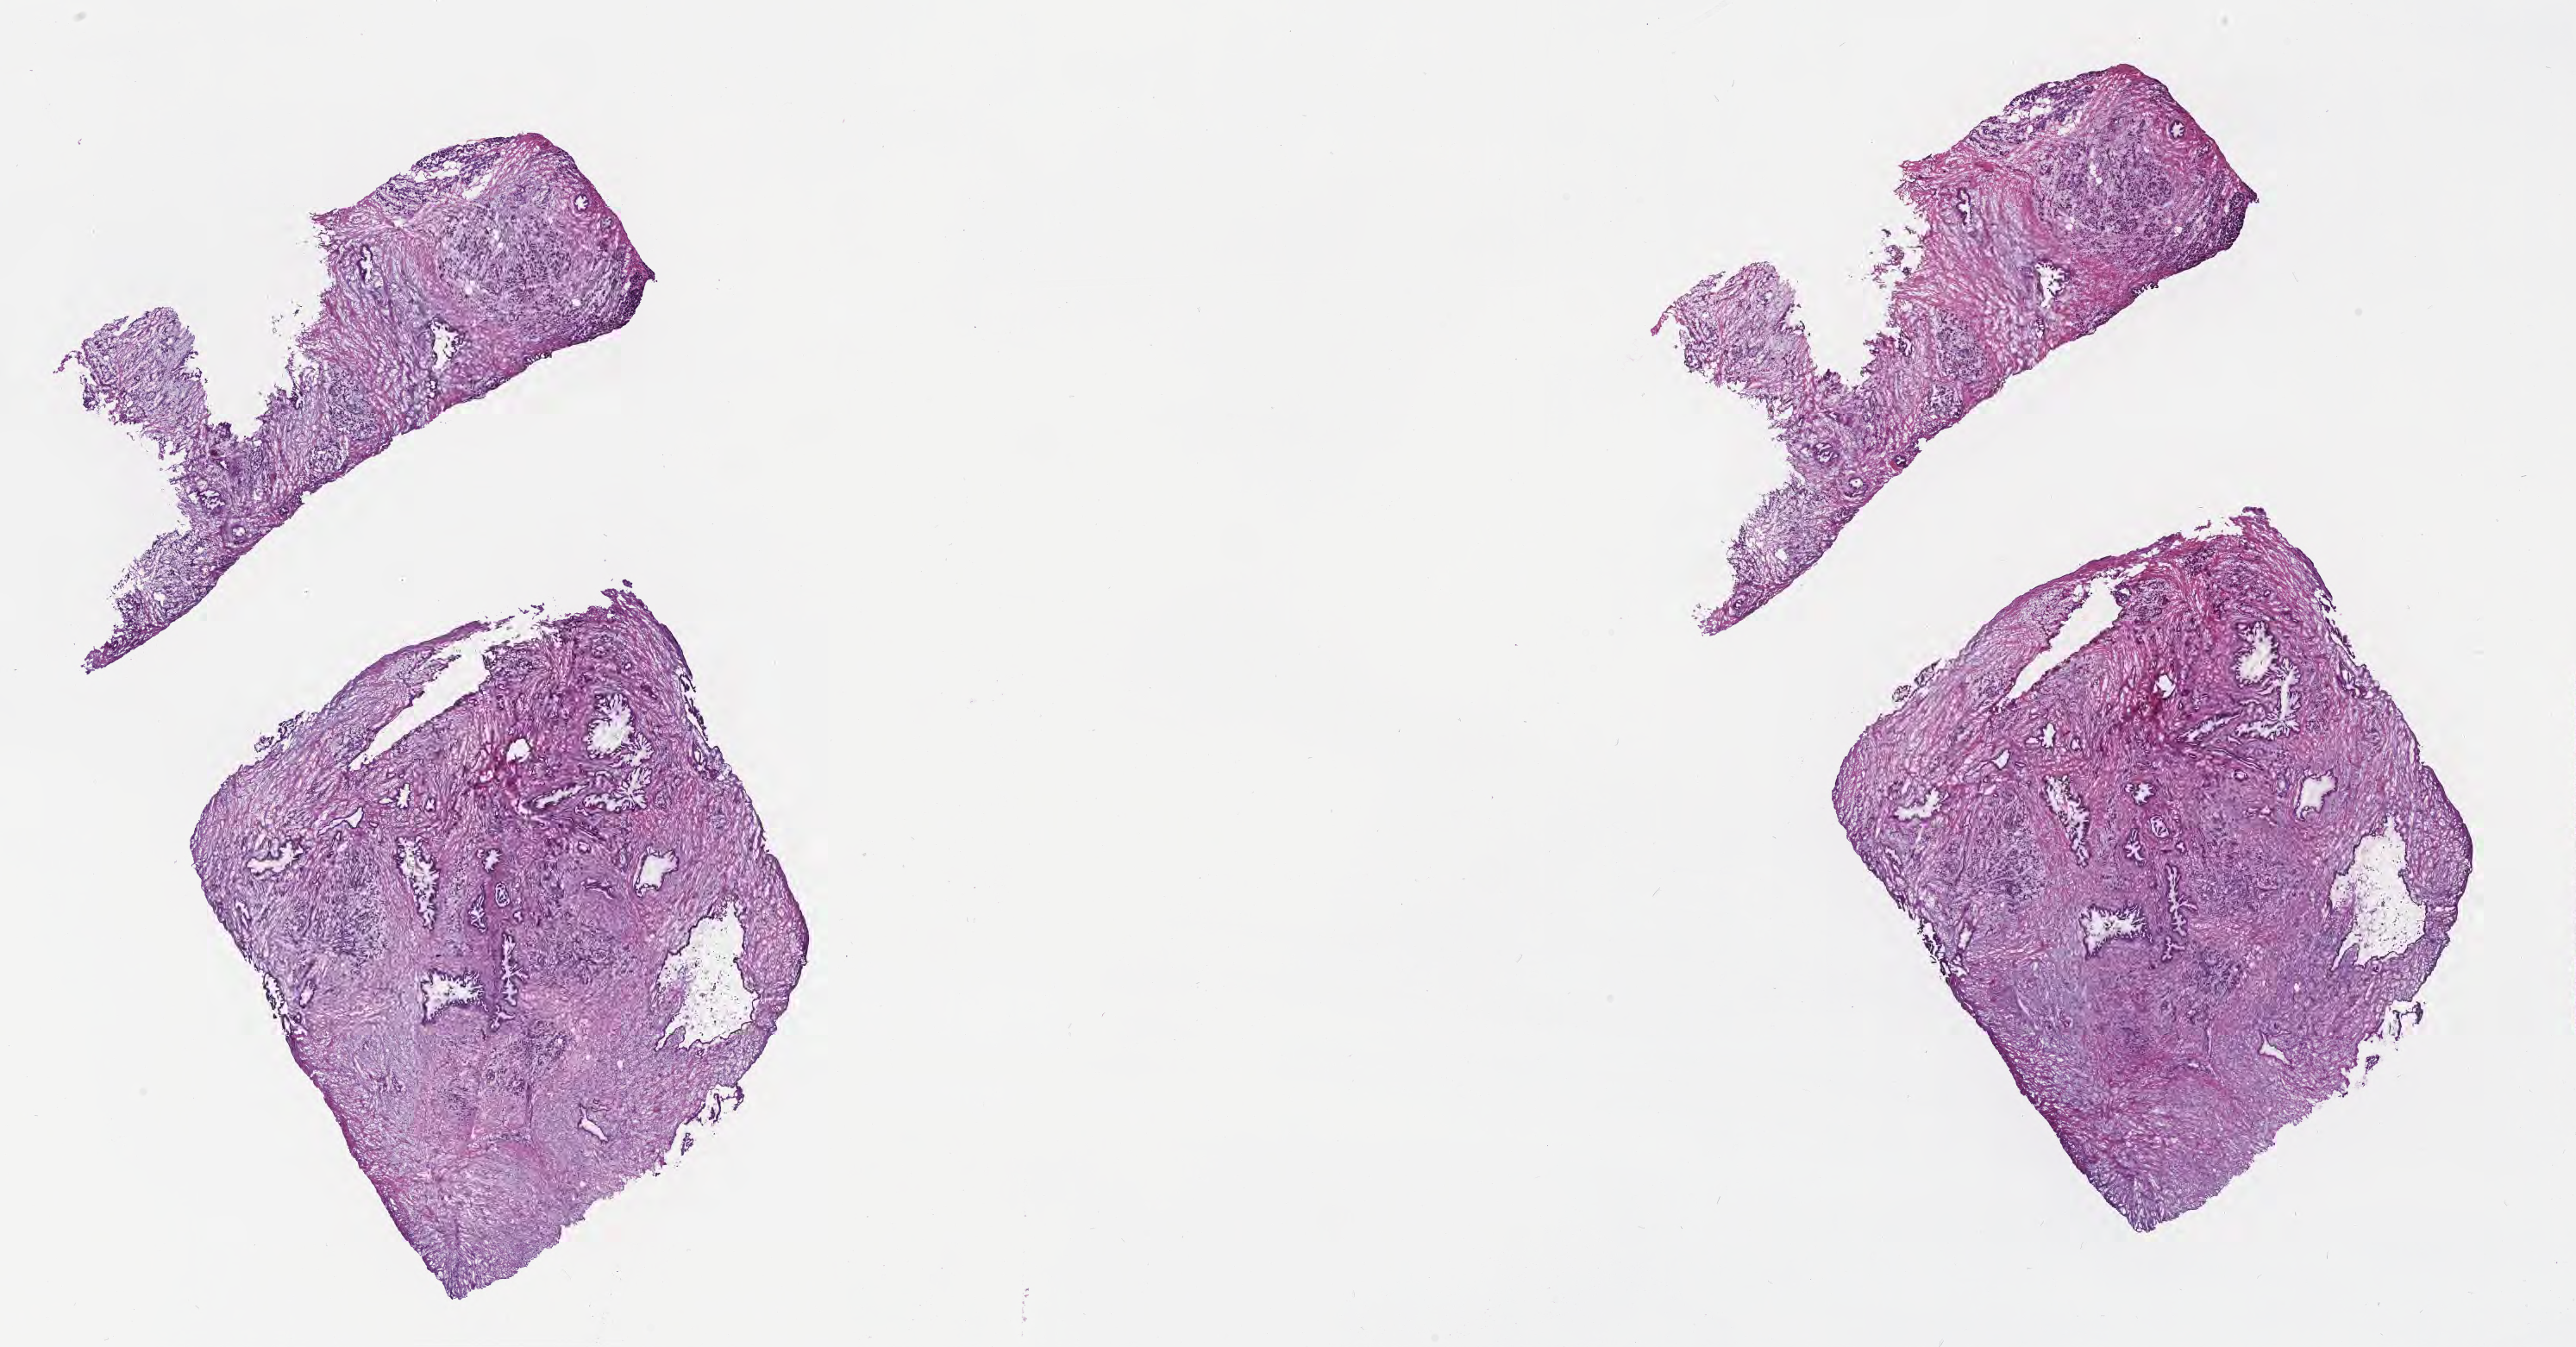
Whole-slide image, hematoxylin and eosin (H&E) stain — shown as a low-resolution overview of the whole scanned area (about 24.2 x 12.6 mm). Frozen section. Primary tumor. Anatomic site: head of pancreas. Male, age 67 years at initial diagnosis. Slide review estimates, as recorded: tumor cells 100%, tumor nuclei 20%, stromal cells 0%, necrosis 0%, normal cells 0%. Infiltration values recorded for this section: lymphocyte infiltration 0%, monocyte infiltration 0%, neutrophil infiltration 0%.
Histologic diagnosis: Infiltrating duct carcinoma, NOS.